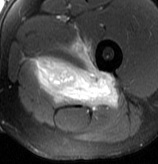
MRI of an extremity soft-tissue mass, one axial slice; position 55 of 70 along the scan axis; T2-weighted fat-saturated; MR volume resampled by the dataset authors to the PET/CT grid (not the native acquisition matrix); 3.27 mm slice thickness; 158 × 164 image matrix. Male patient. From the clinical record (not read from this slice): histological type: extraskeletal osteosarcoma; grade: high; site of the primary tumour: left adductur.
Annotated regions visible in this slice (expert contour drawn on MRI and transferred to this co-registered scan by the dataset authors):
- gross tumour volume (mass): bounding box (x1, y1, x2, y2) in pixels: (31, 37, 119, 111)